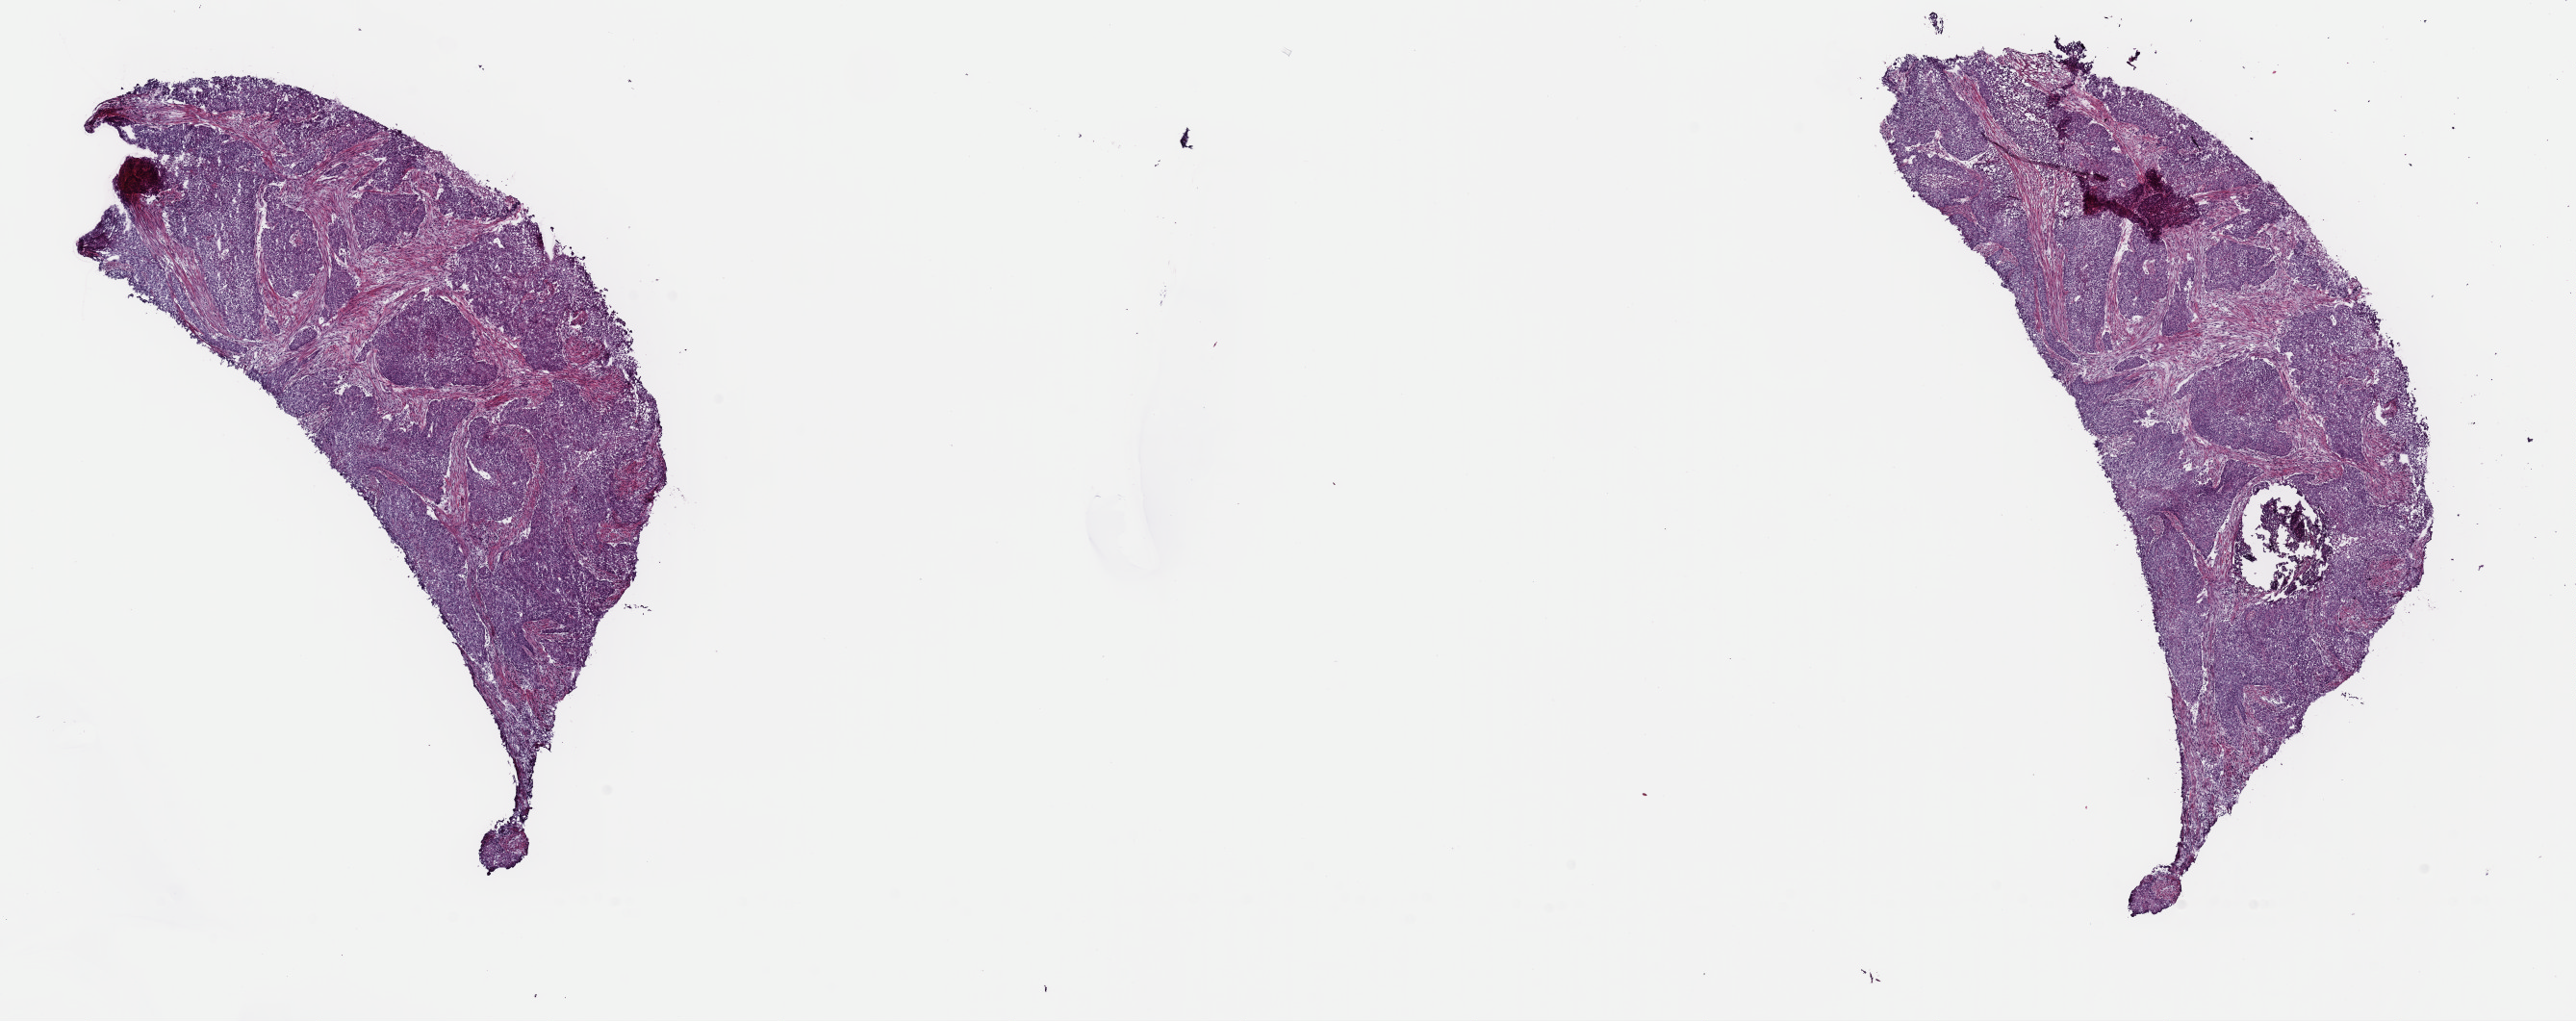
H&E-stained whole-slide image, a low-resolution overview of the entire scanned area, about 21.1 x 8.4 mm (from a 40x scan); frozen section from the top of the tissue portion; uterus, primary tumour sample. Female, age 87 years at initial diagnosis. Slide review estimates, as recorded: tumour cells 75%, tumour nuclei 75%.
Diagnosis: Endometrioid adenocarcinoma, NOS.